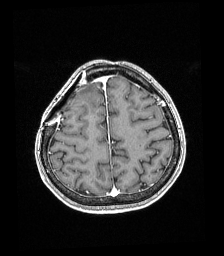
Brain MRI from a brain-tumour surgery series, one axial slice. Position 54 of 192 along the scan axis. T1-weighted post-contrast. 1 mm slice thickness. 224 × 256 image matrix, field of view 219 × 250 mm. Case-level facts recorded for this patient, not image findings: histopathology: Astrocytoma; WHO grade: 4; IDH mutation: yes.
Outlined on this slice (outlined manually by an expert reader):
- tumour: bounding box (x1, y1, x2, y2) in pixels: (81, 92, 83, 94)